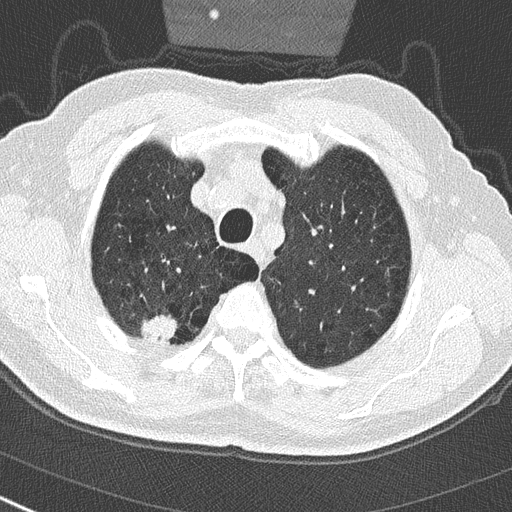
Low-dose screening chest CT, one axial slice. Position 239 of 290 along the scan axis. 120 kVp. Lung window (W 1500 / L -600 HU). 512 × 512 image matrix, field of view 300 × 300 mm.
Annotated regions visible in this slice (expert manual segmentation):
- lesion 1 (tumor, upper lobe of right lung): bounding box [x1, y1, x2, y2] px = [139, 314, 178, 341]